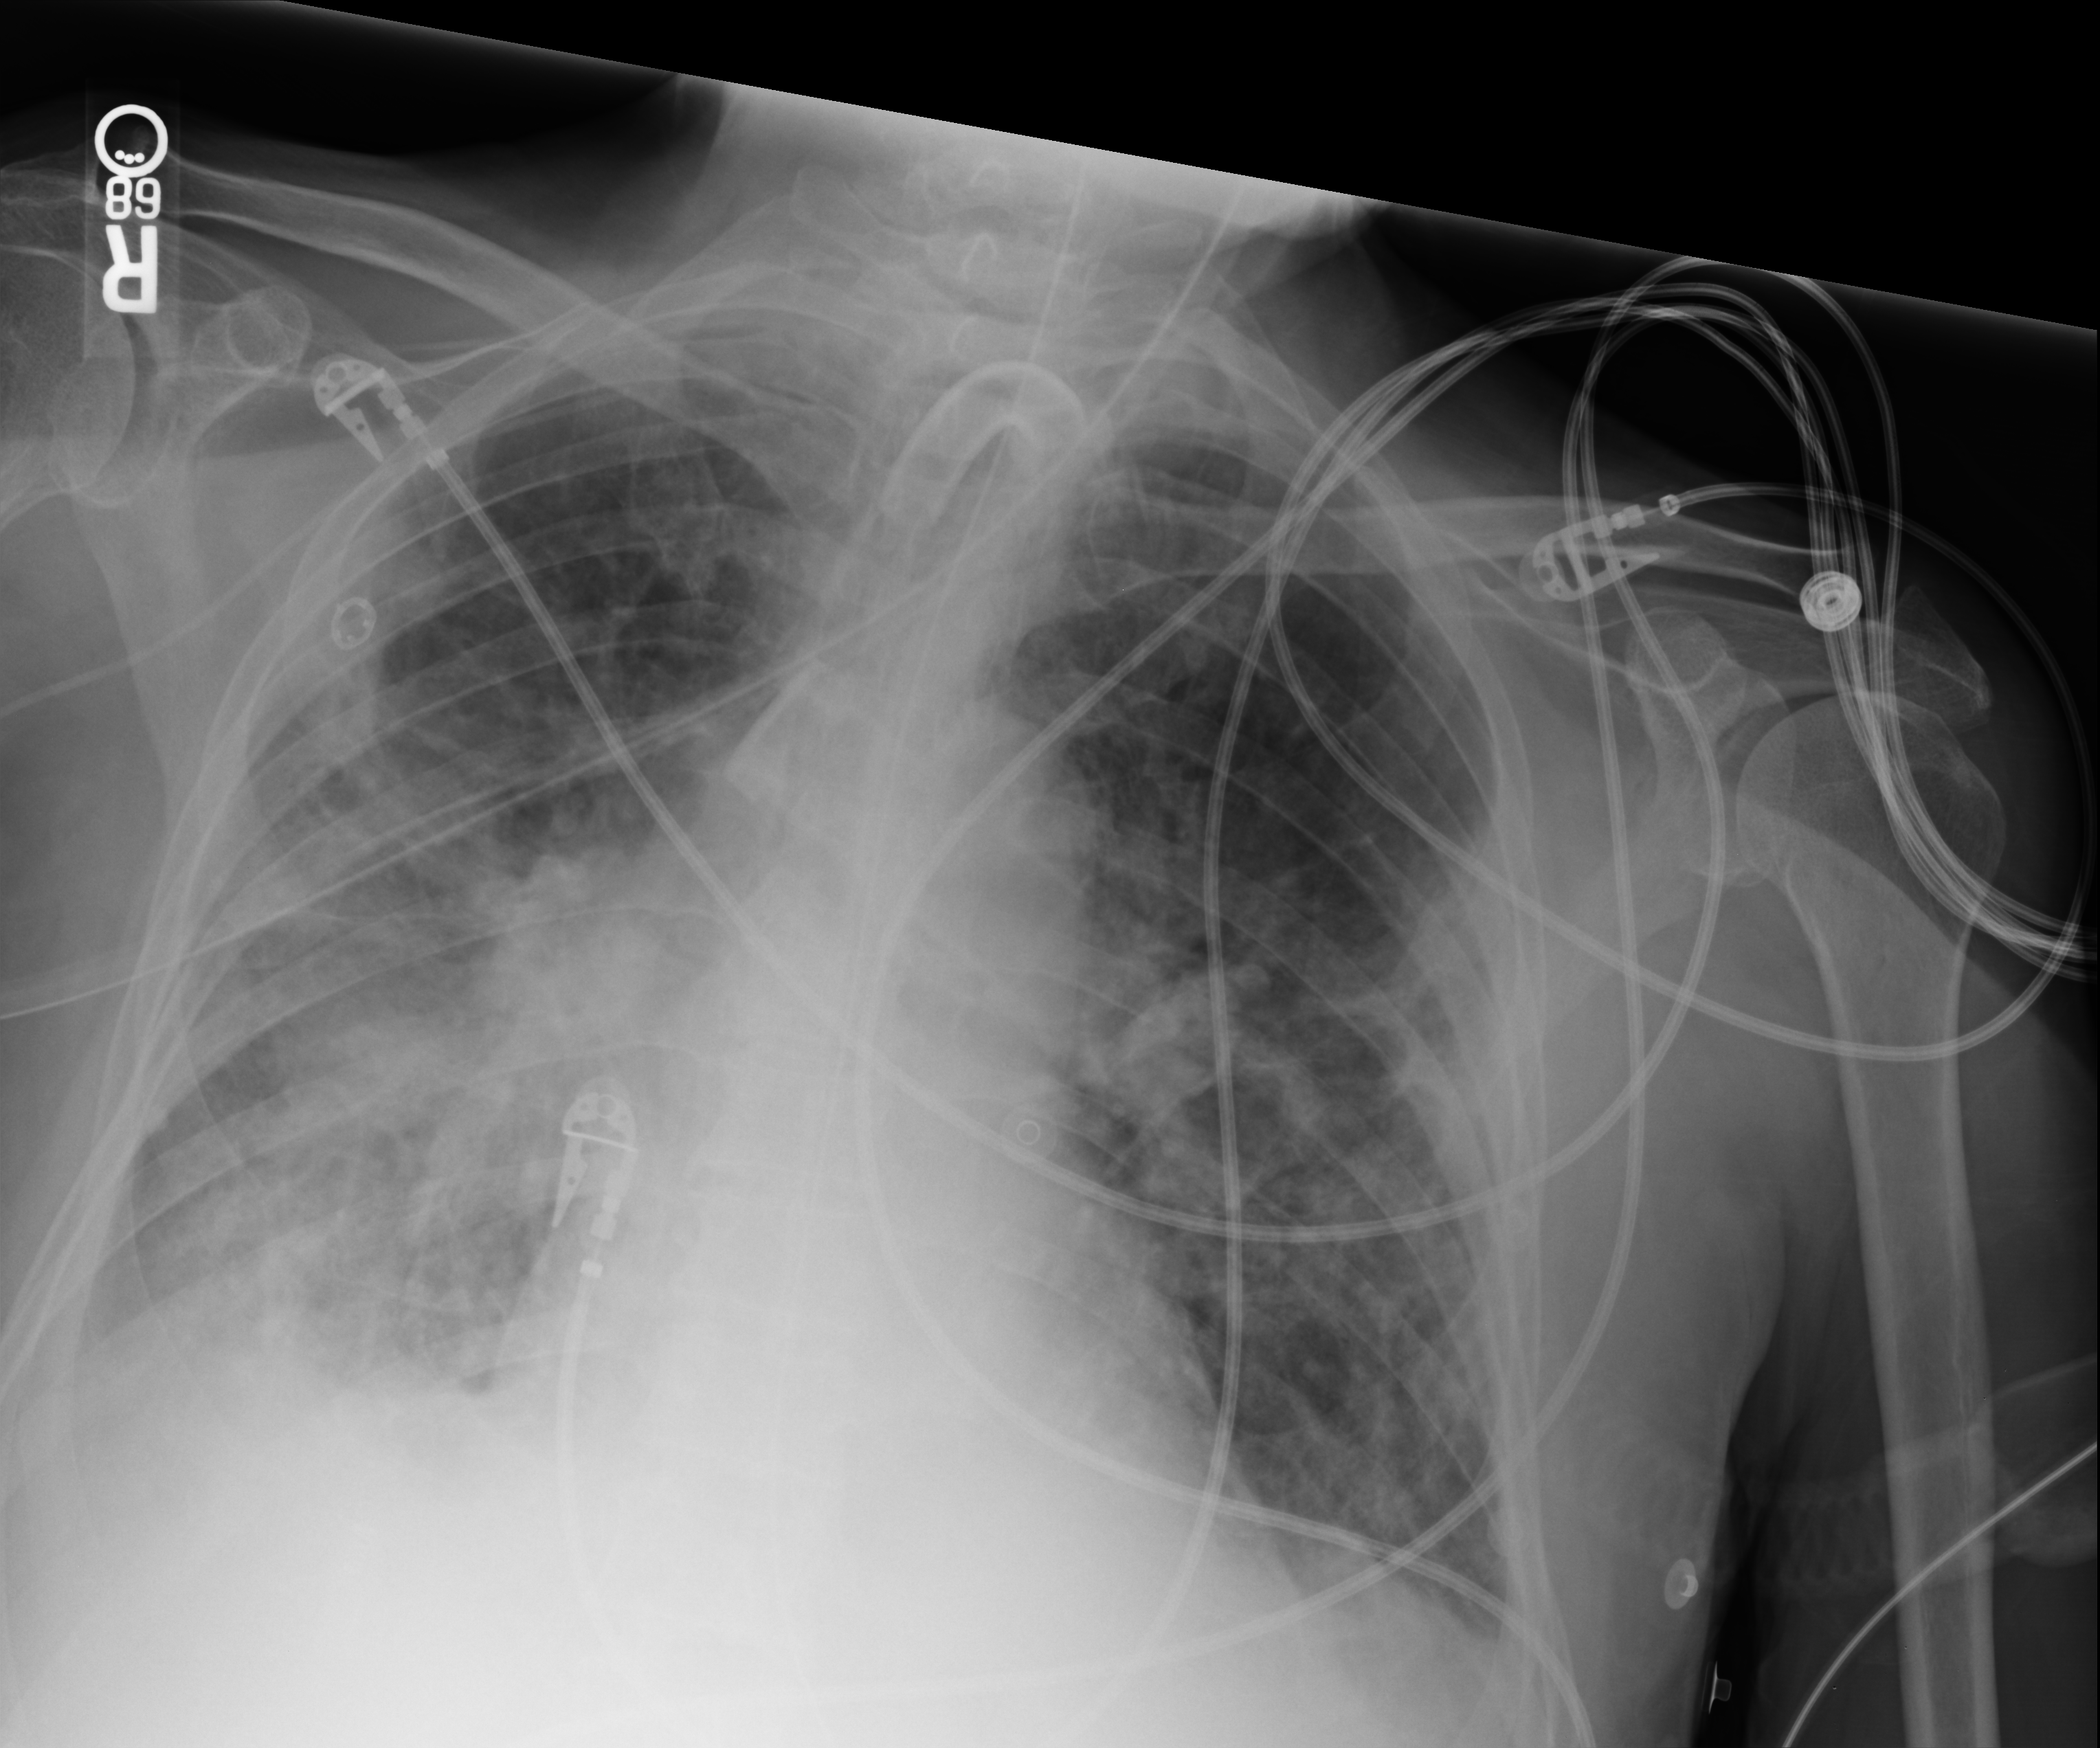
Chest X-ray (portable). Male patient hospitalised with COVID-19, age 75–90 years.
From the hospital-stay record, not from the radiograph (when in the stay this image was taken is not recorded): diabetes (admission record): no; mechanically ventilated during this hospital stay: yes.